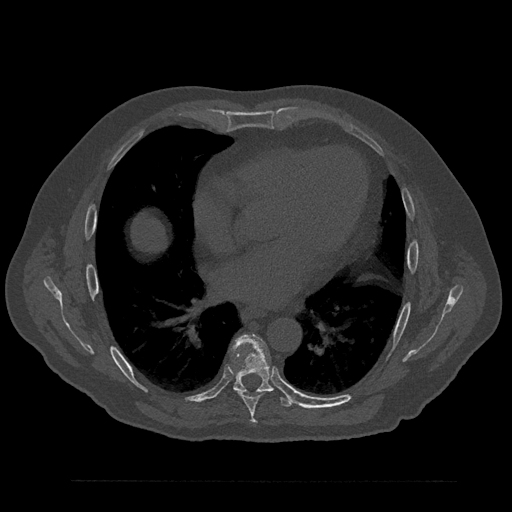
CT including the spine, one axial slice; slice 481 of 797 in the series (ordered by position); reconstruction kernel Br40s/3; bone window (W 1800 / L 400 HU); 0.5 mm slice thickness; 512 × 512 image matrix, field of view 430 × 430 mm. Patient: male, 61 years. From the clinical record (not read from this slice): primary cancer: prostate.
Outlined on this slice (semi-automatic segmentation, software-assisted and operator-edited):
- T7 vertebra: box from (x=236, y=391) to (x=262, y=424) px
- T8 vertebra: (x=232, y=335)–(x=294, y=407)